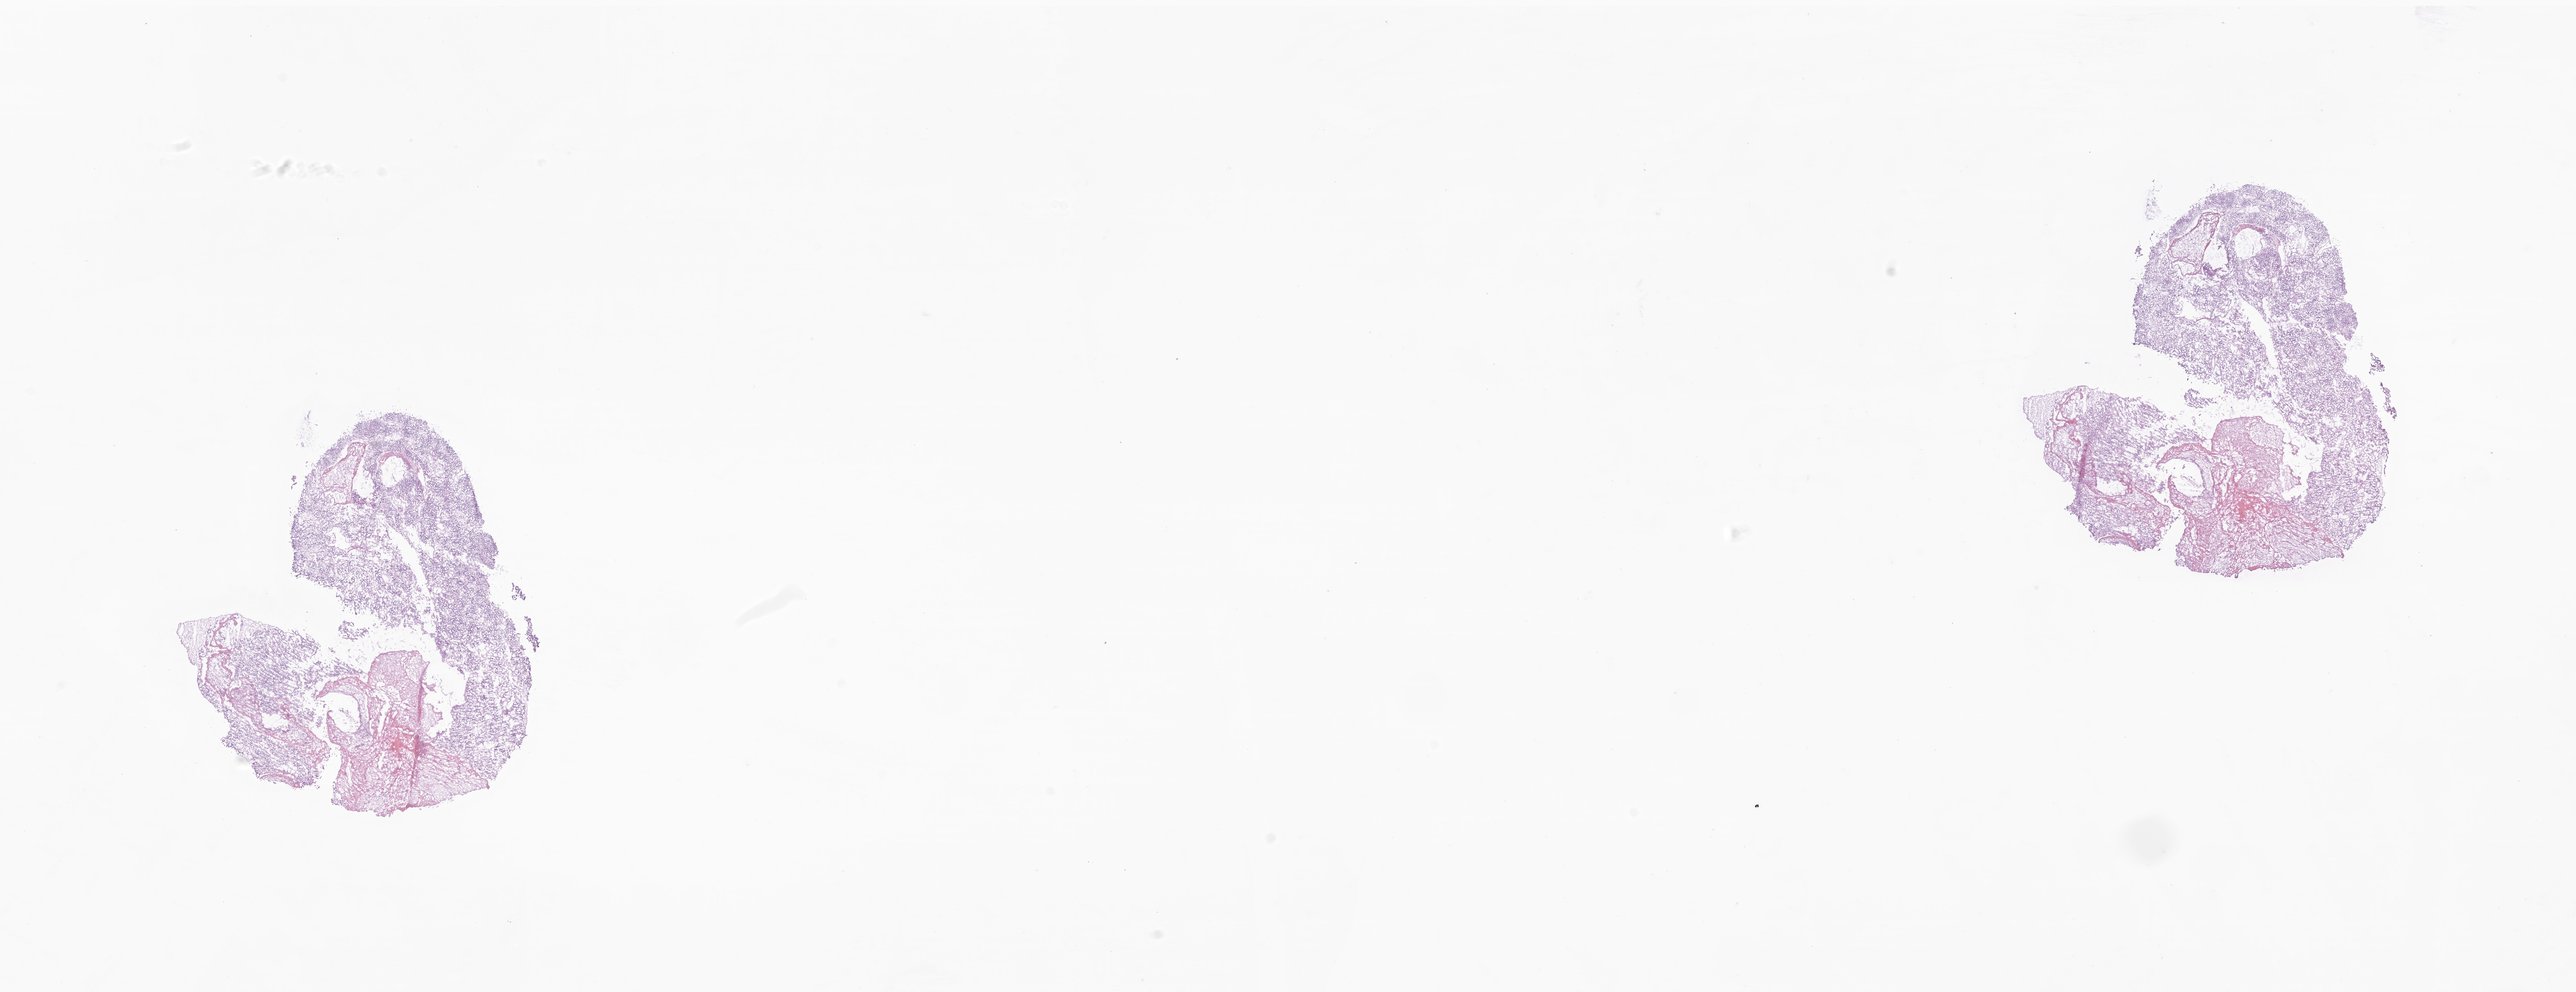
H&E whole-slide image of tumor tissue from the parietal lobe — shown as a low-resolution overview of the whole scanned area (about 26.5 x 10.2 mm), frozen section. Patient: male, age 70 months (5 years 10 months).
• diagnosis: Neoplasm, malignant